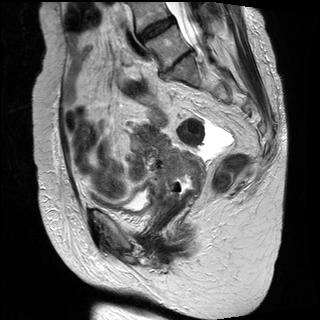
Pelvic MRI for cervical cancer, one sagittal slice; slice 12 of 30 in the series (ordered by position); T2-weighted; 1.5 T; TE 89 ms, TR 2930 ms; 4 mm slice thickness; 320 × 320 image matrix. Female patient, age 61 years.
Structures marked on this image (expert manual segmentation):
- uterus and cervix: bounding box <129,124,206,220> (left, top, right, bottom; pixels)